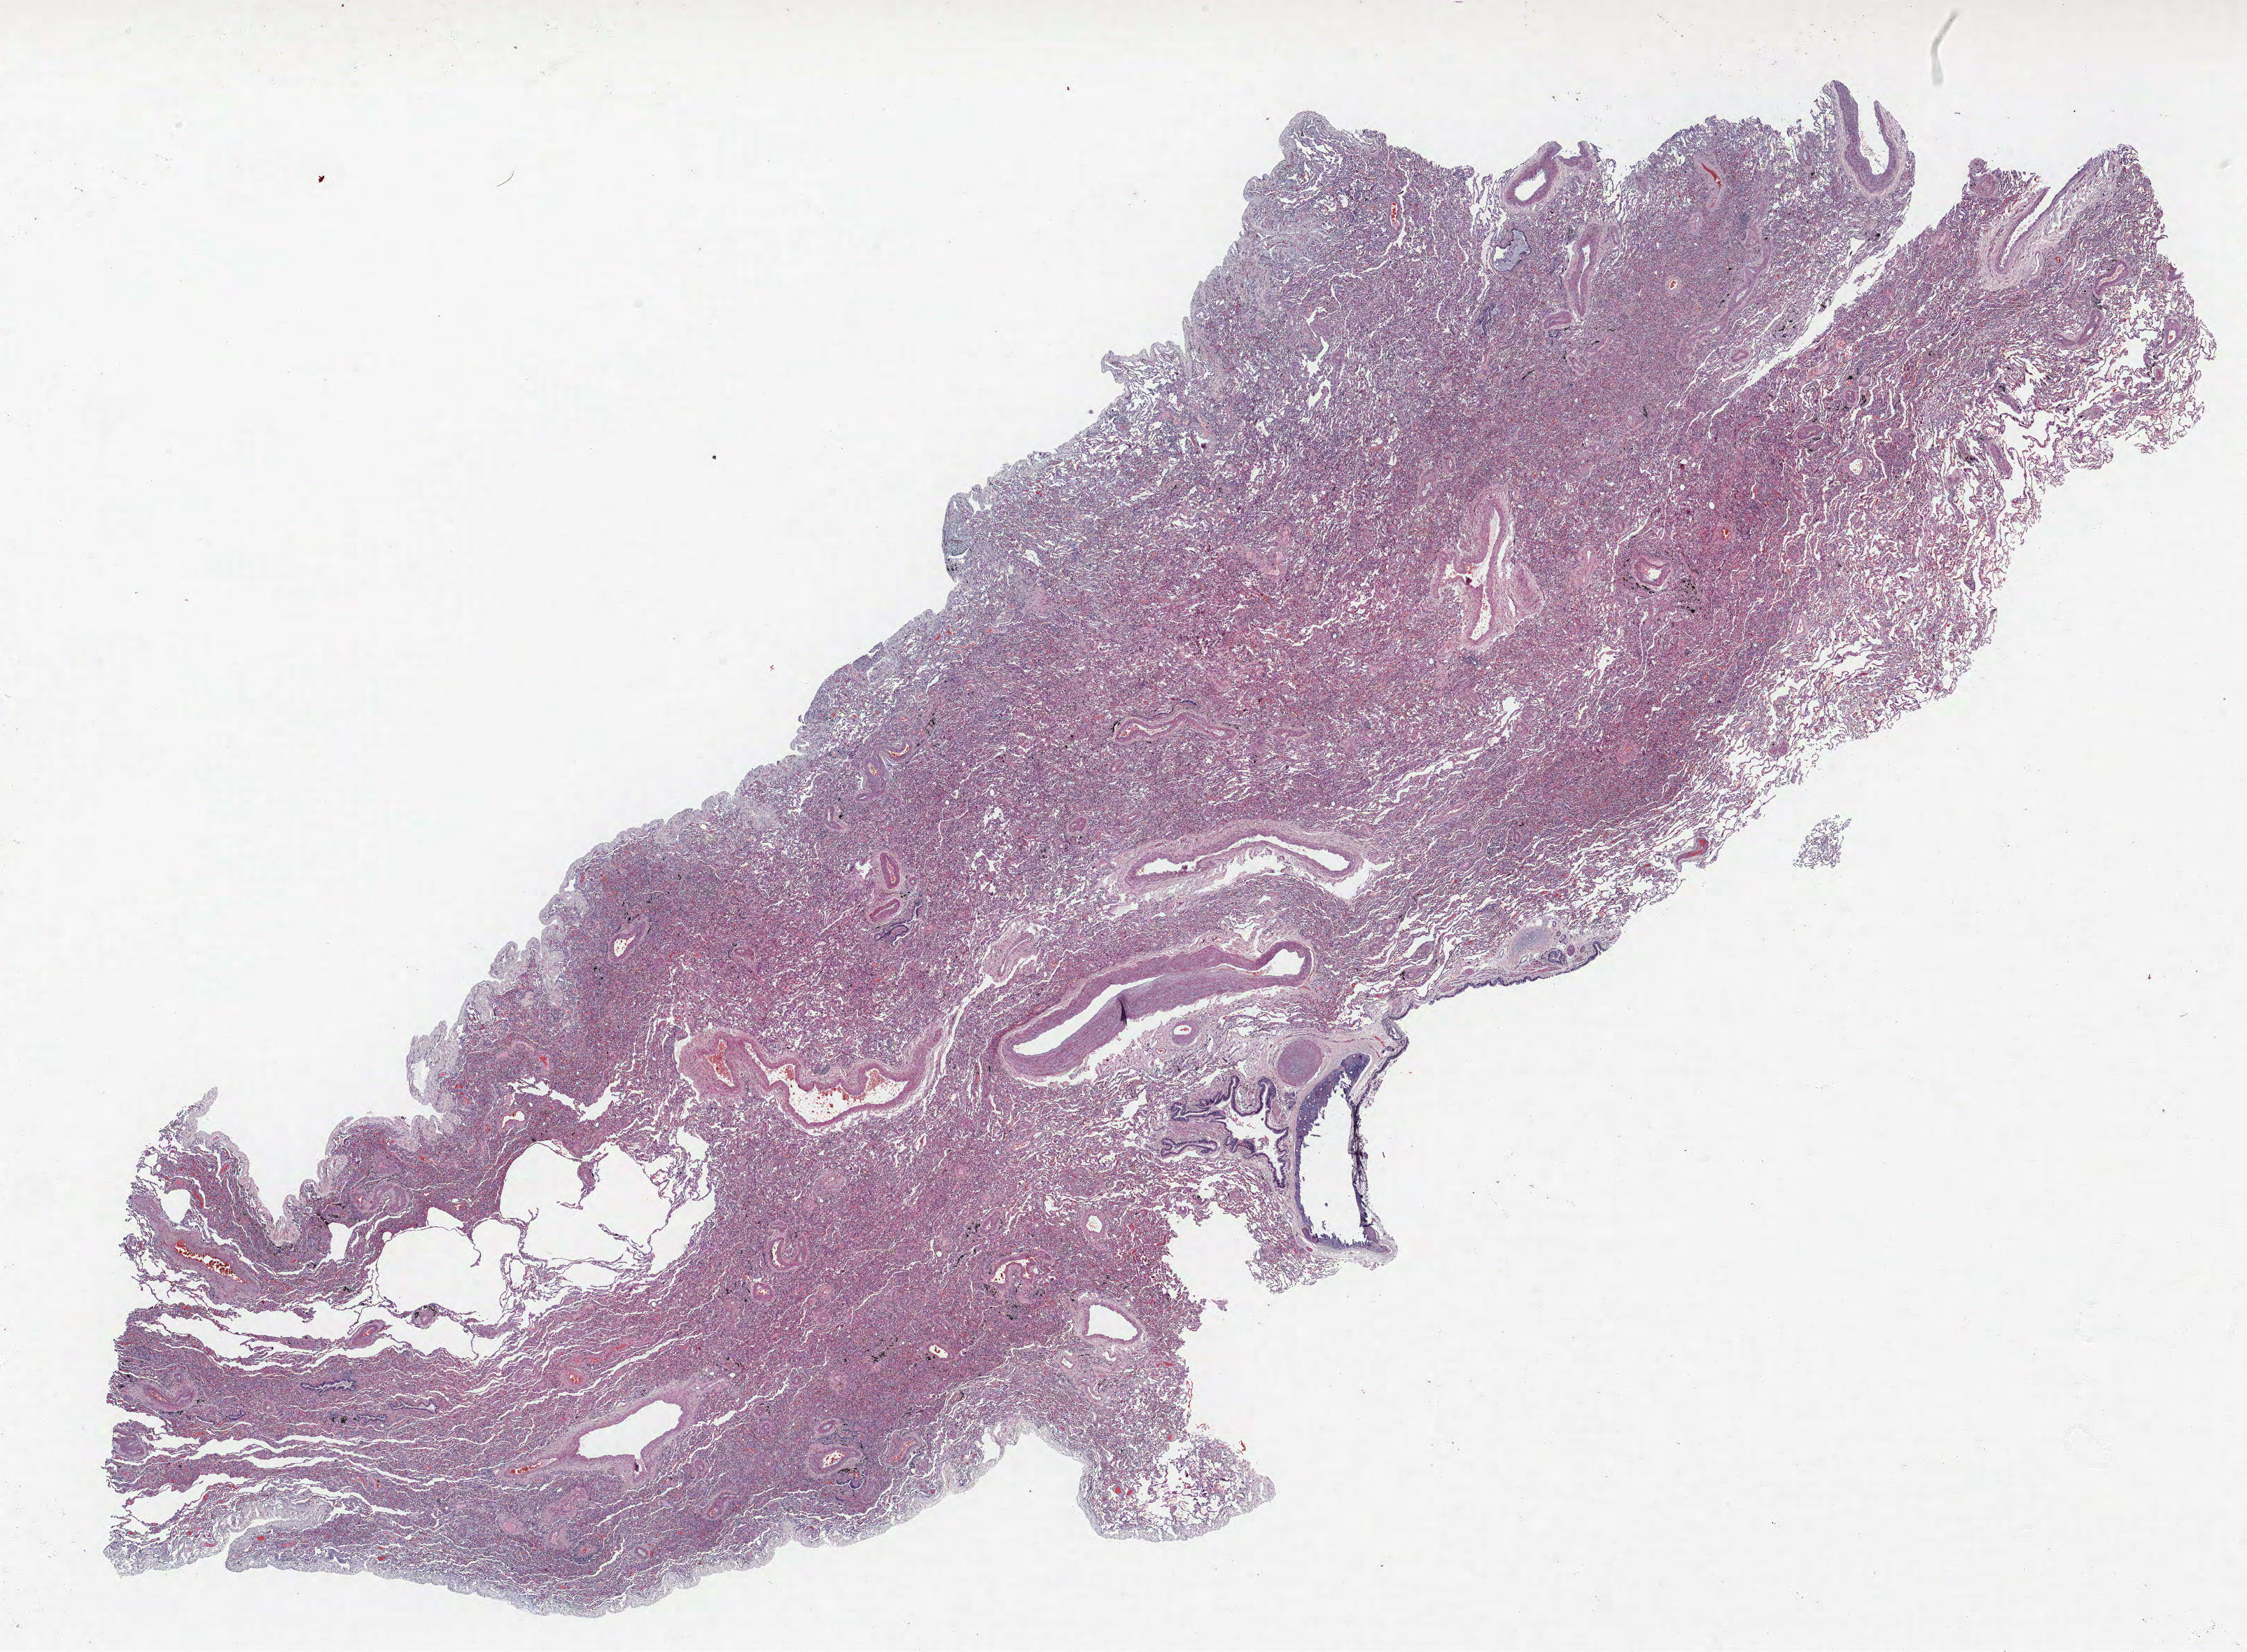
Whole-slide histology image, H&E-stained, low-resolution overview of the scanned area, about 25.7 x 18.9 mm. FFPE section. Lung. Male, age 61 at enrolment. Former smoker at enrolment.
Participant's lung-cancer diagnosis: Adenocarcinoma, NOS.